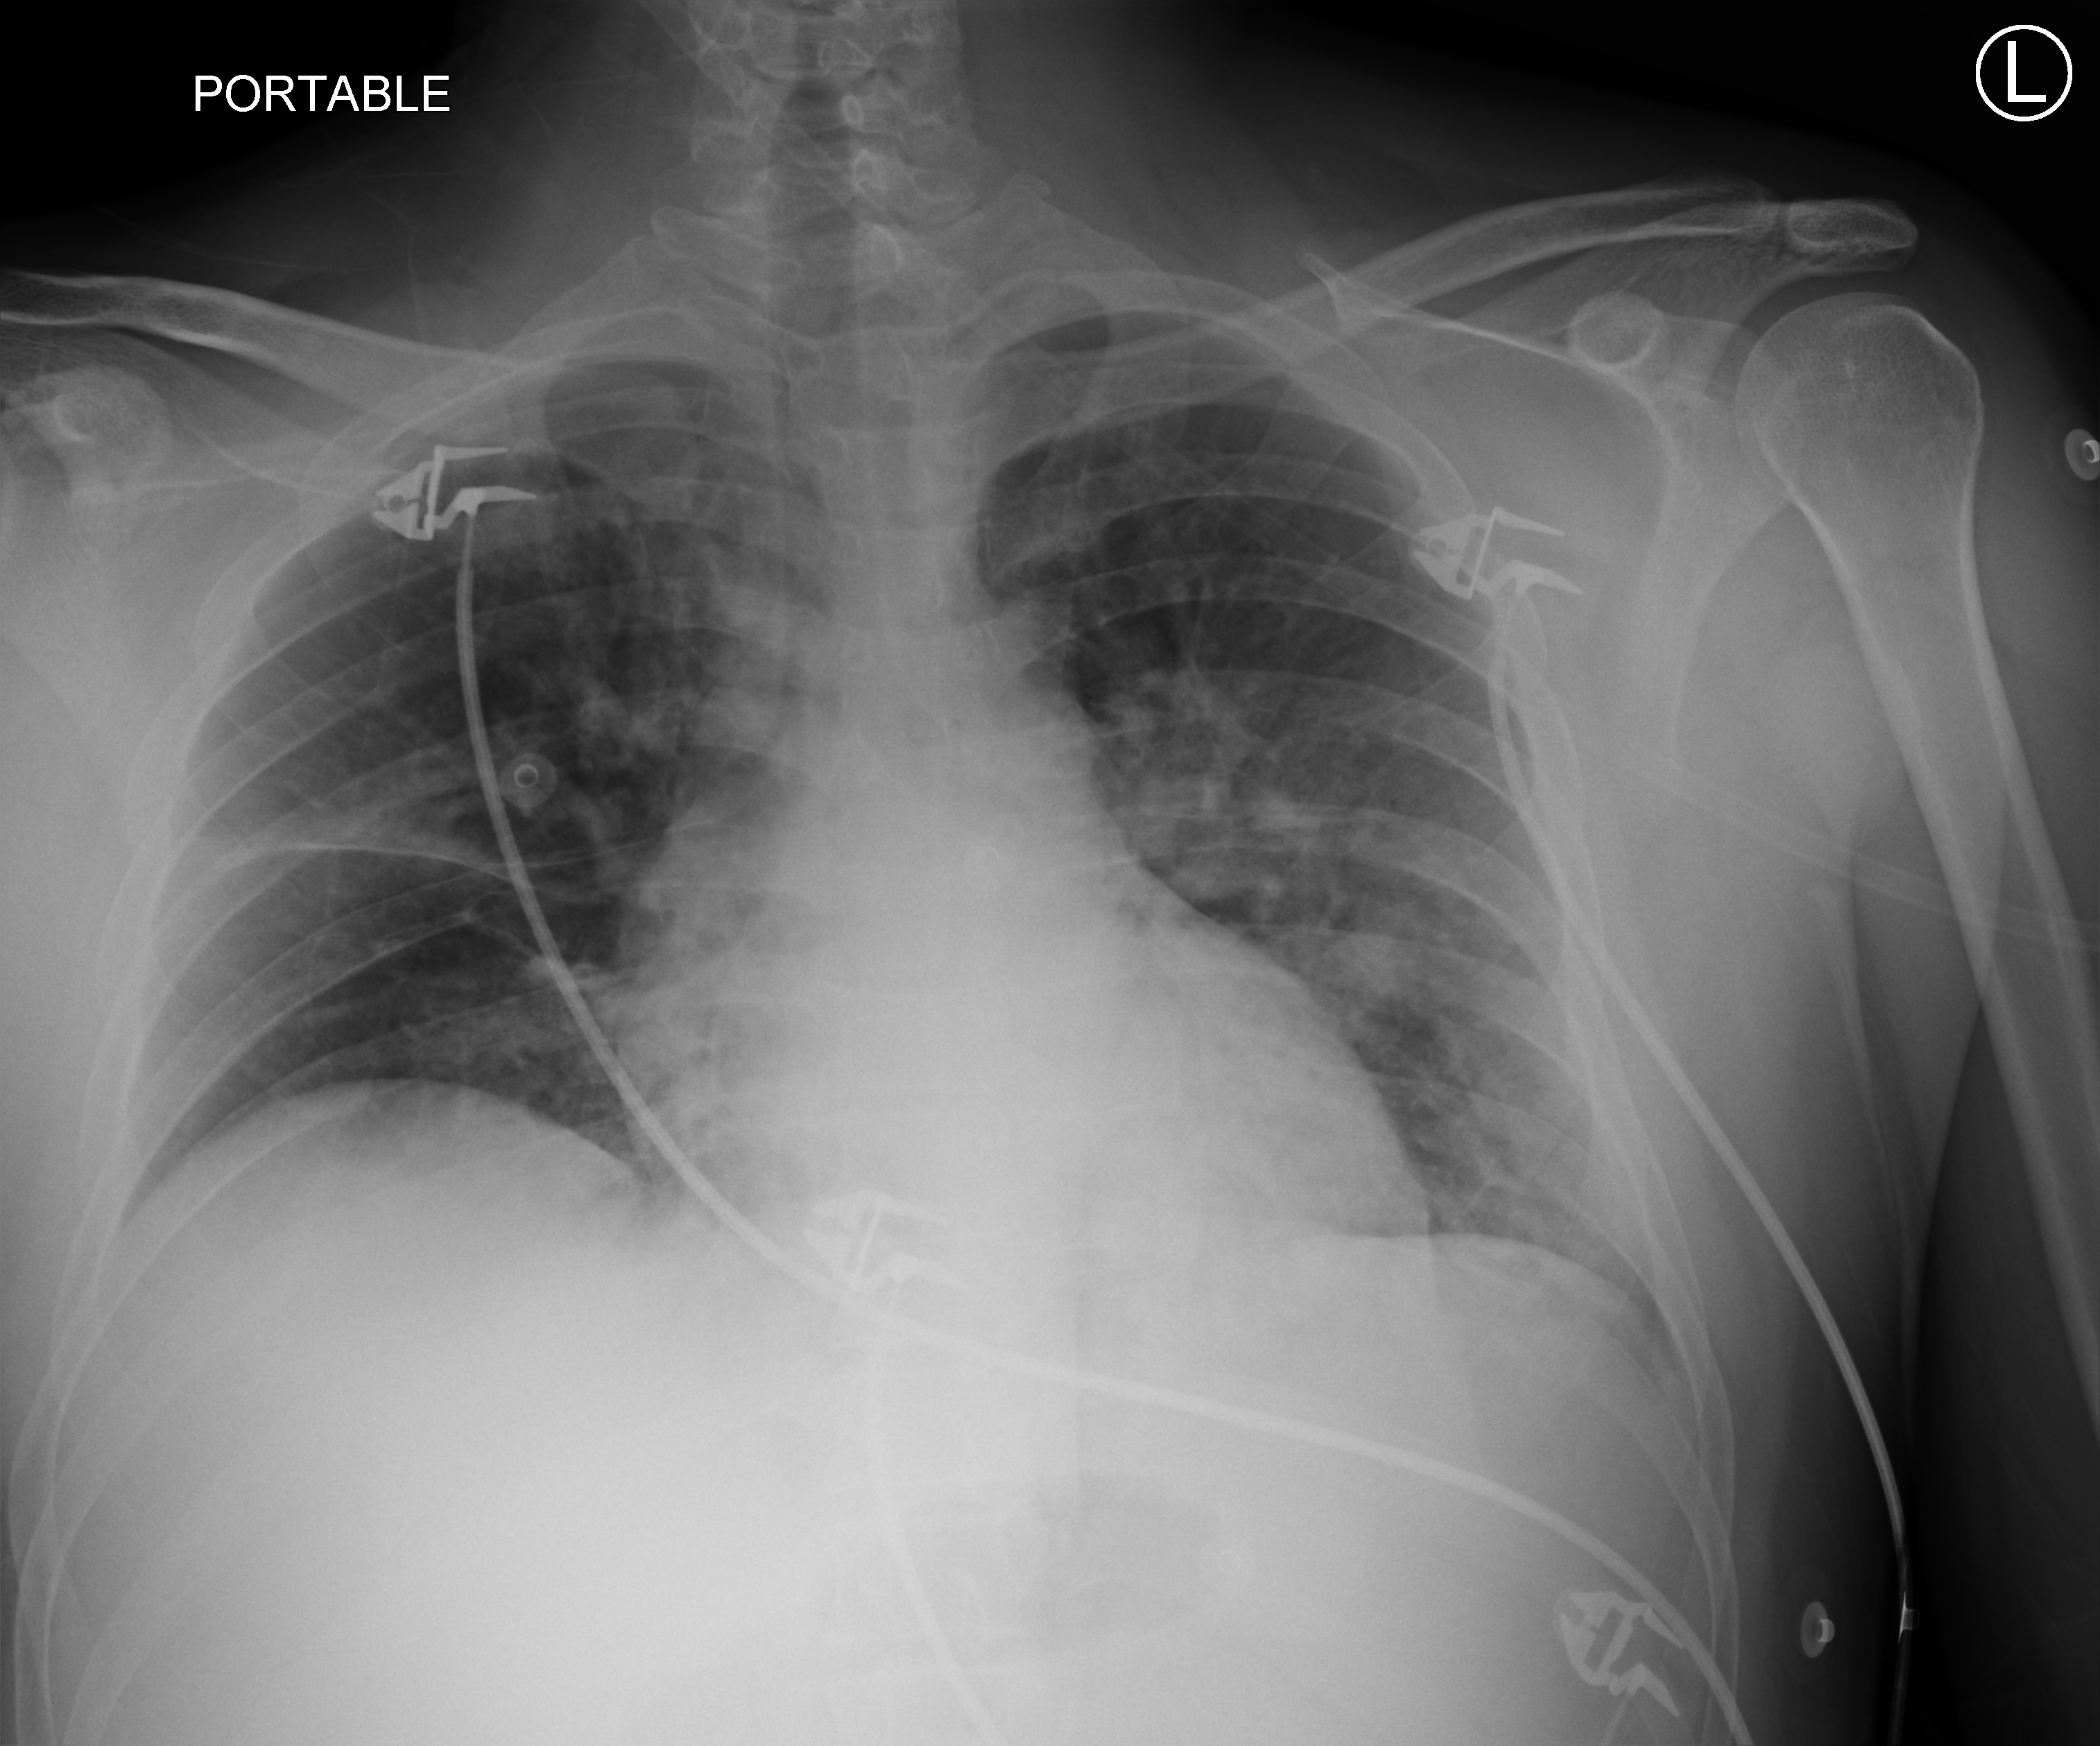
Bedside chest radiograph (computed radiography). Patient hospitalised with COVID-19, aged 18–59 years.
From the hospital-stay record, not from the radiograph (when in the stay this image was taken is not recorded): other chronic lung disease (admission record): no; mechanically ventilated during this hospital stay: yes; diabetes (admission record): no.